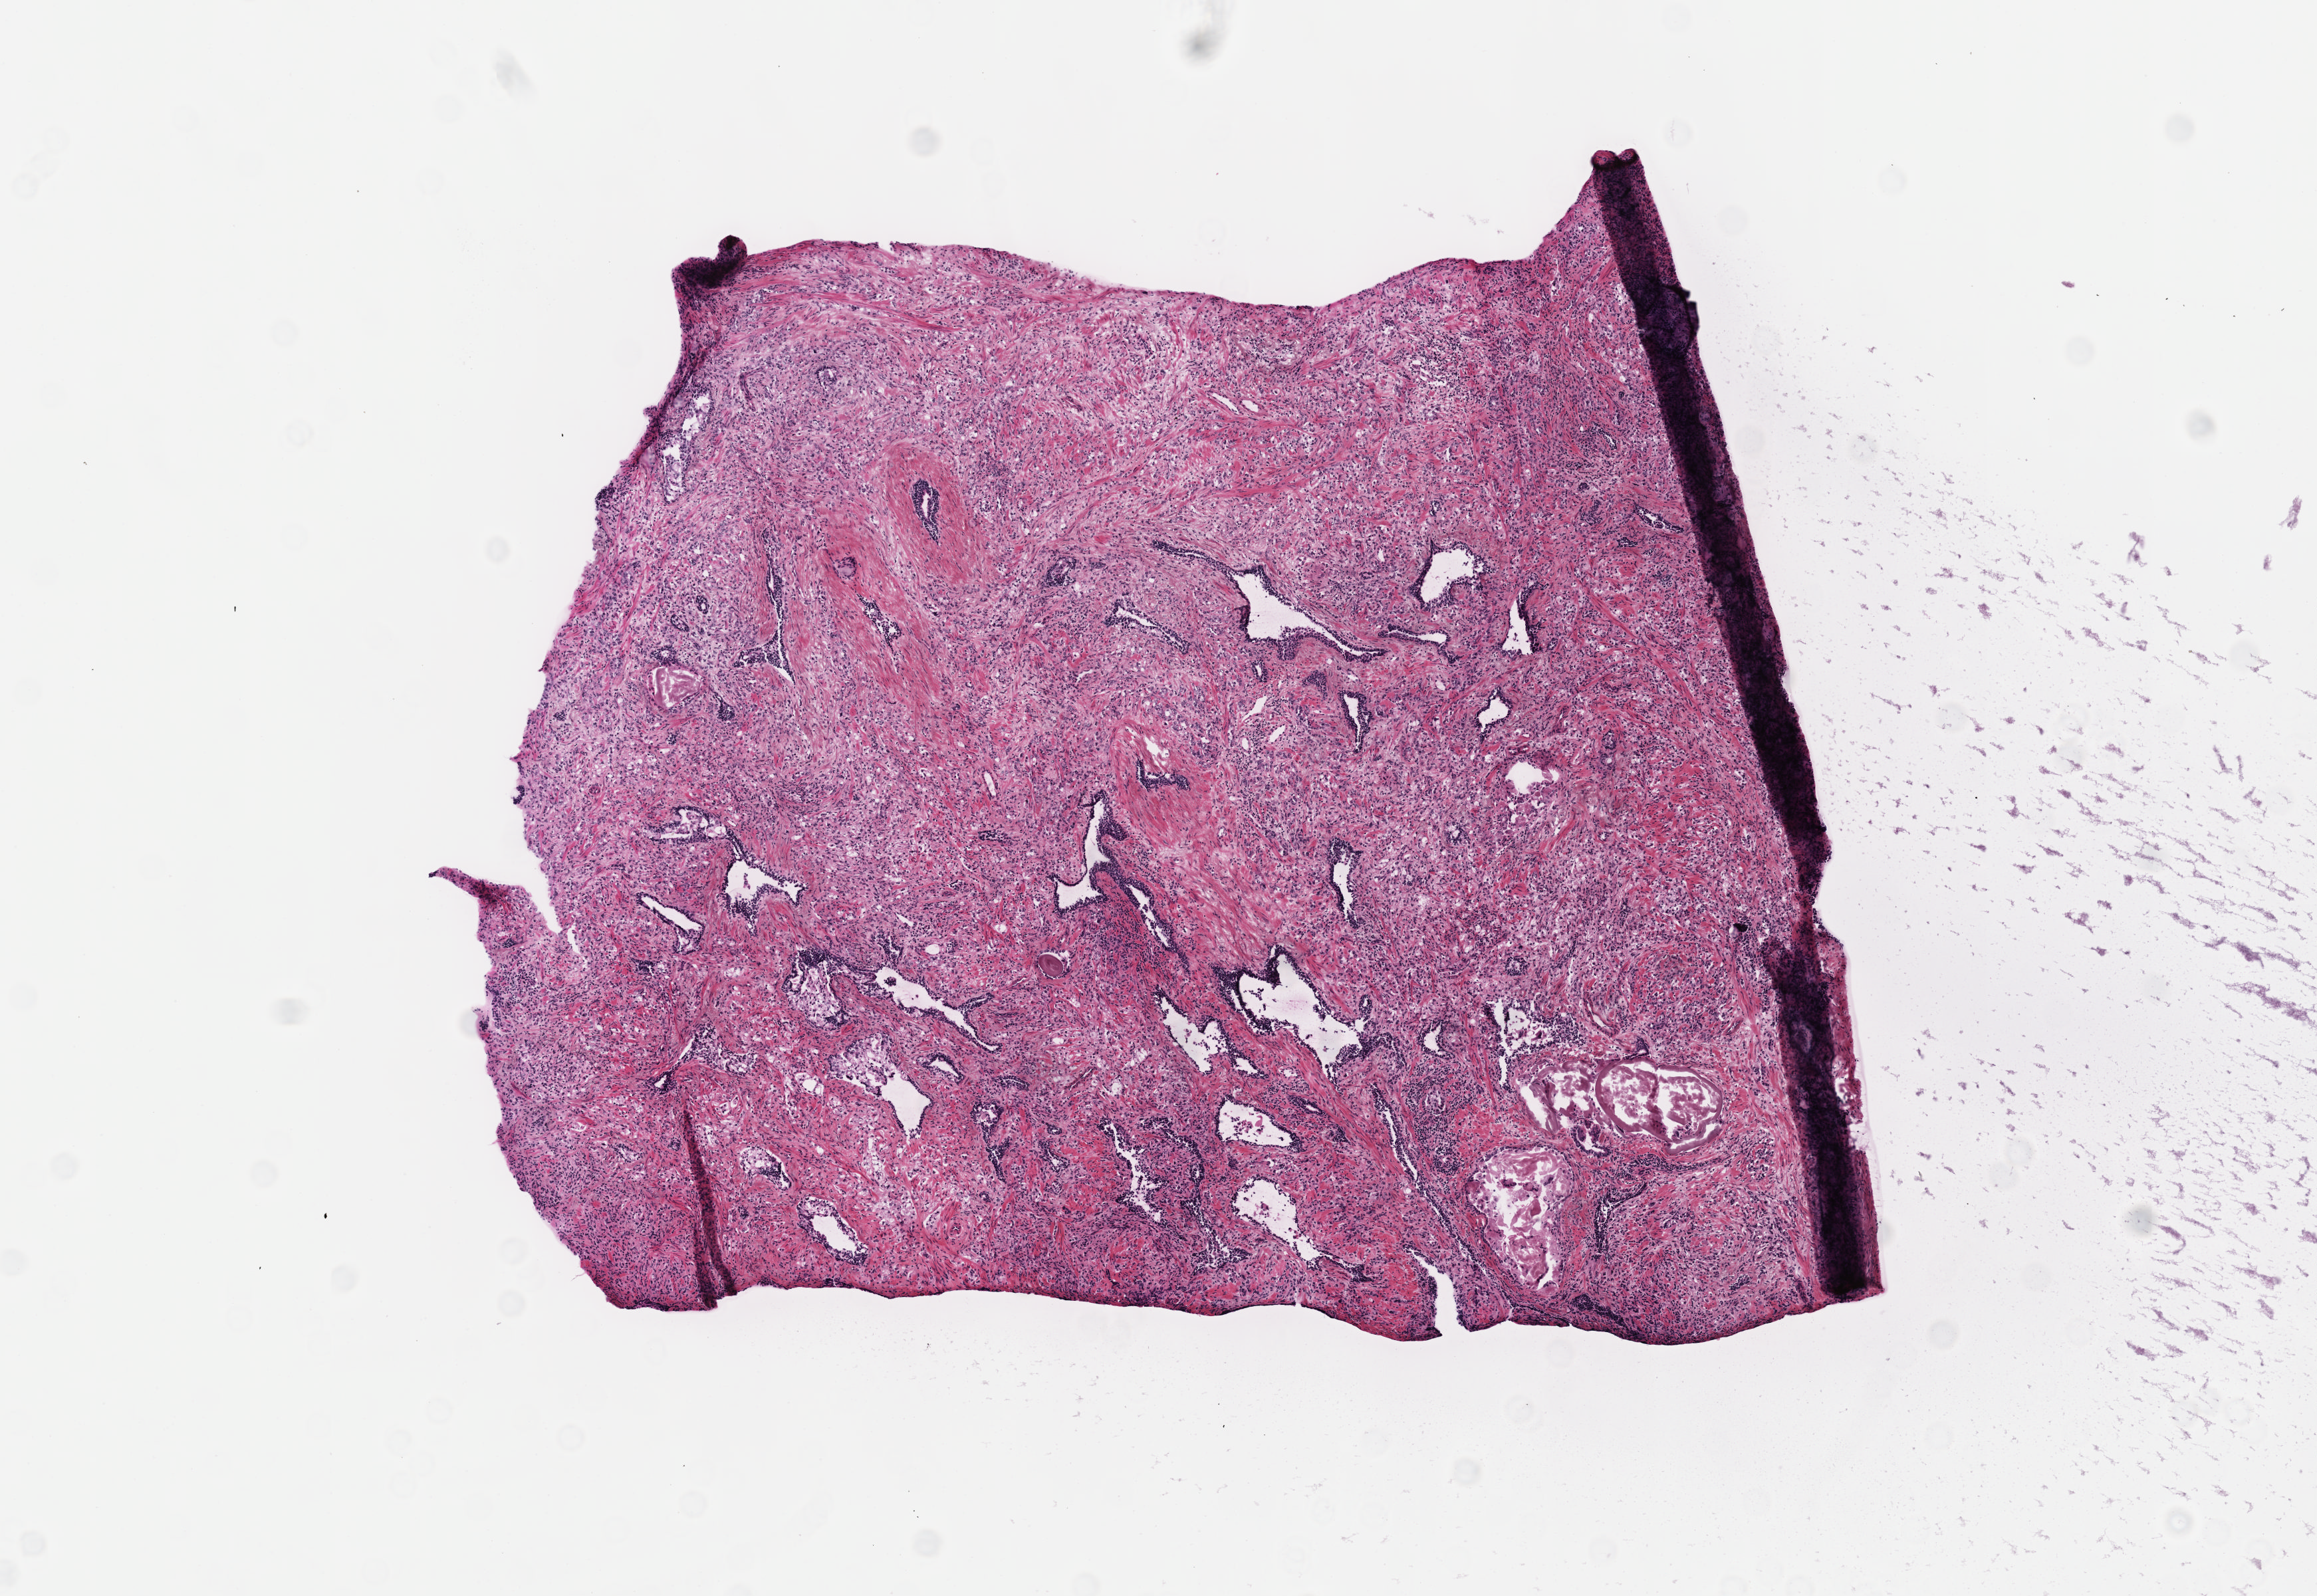
Hematoxylin and eosin (H&E) stained whole-slide image, whole scanned area (about 7.0 x 4.9 mm) shown as a low-resolution overview, frozen section from the top of the tissue portion, prostate, primary tumour sample. Male patient; age at initial diagnosis 62 years. Gleason score: 9 (5+4). Slide review estimates, as recorded: tumour cells 44%, tumour nuclei 60%, normal cells 15%, stromal cells 40%, necrosis 1%. Inflammatory infiltration, as recorded: lymphocyte infiltration 15%, monocyte infiltration 2%, neutrophil infiltration 2%.
* pathologic diagnosis: Adenocarcinoma, NOS